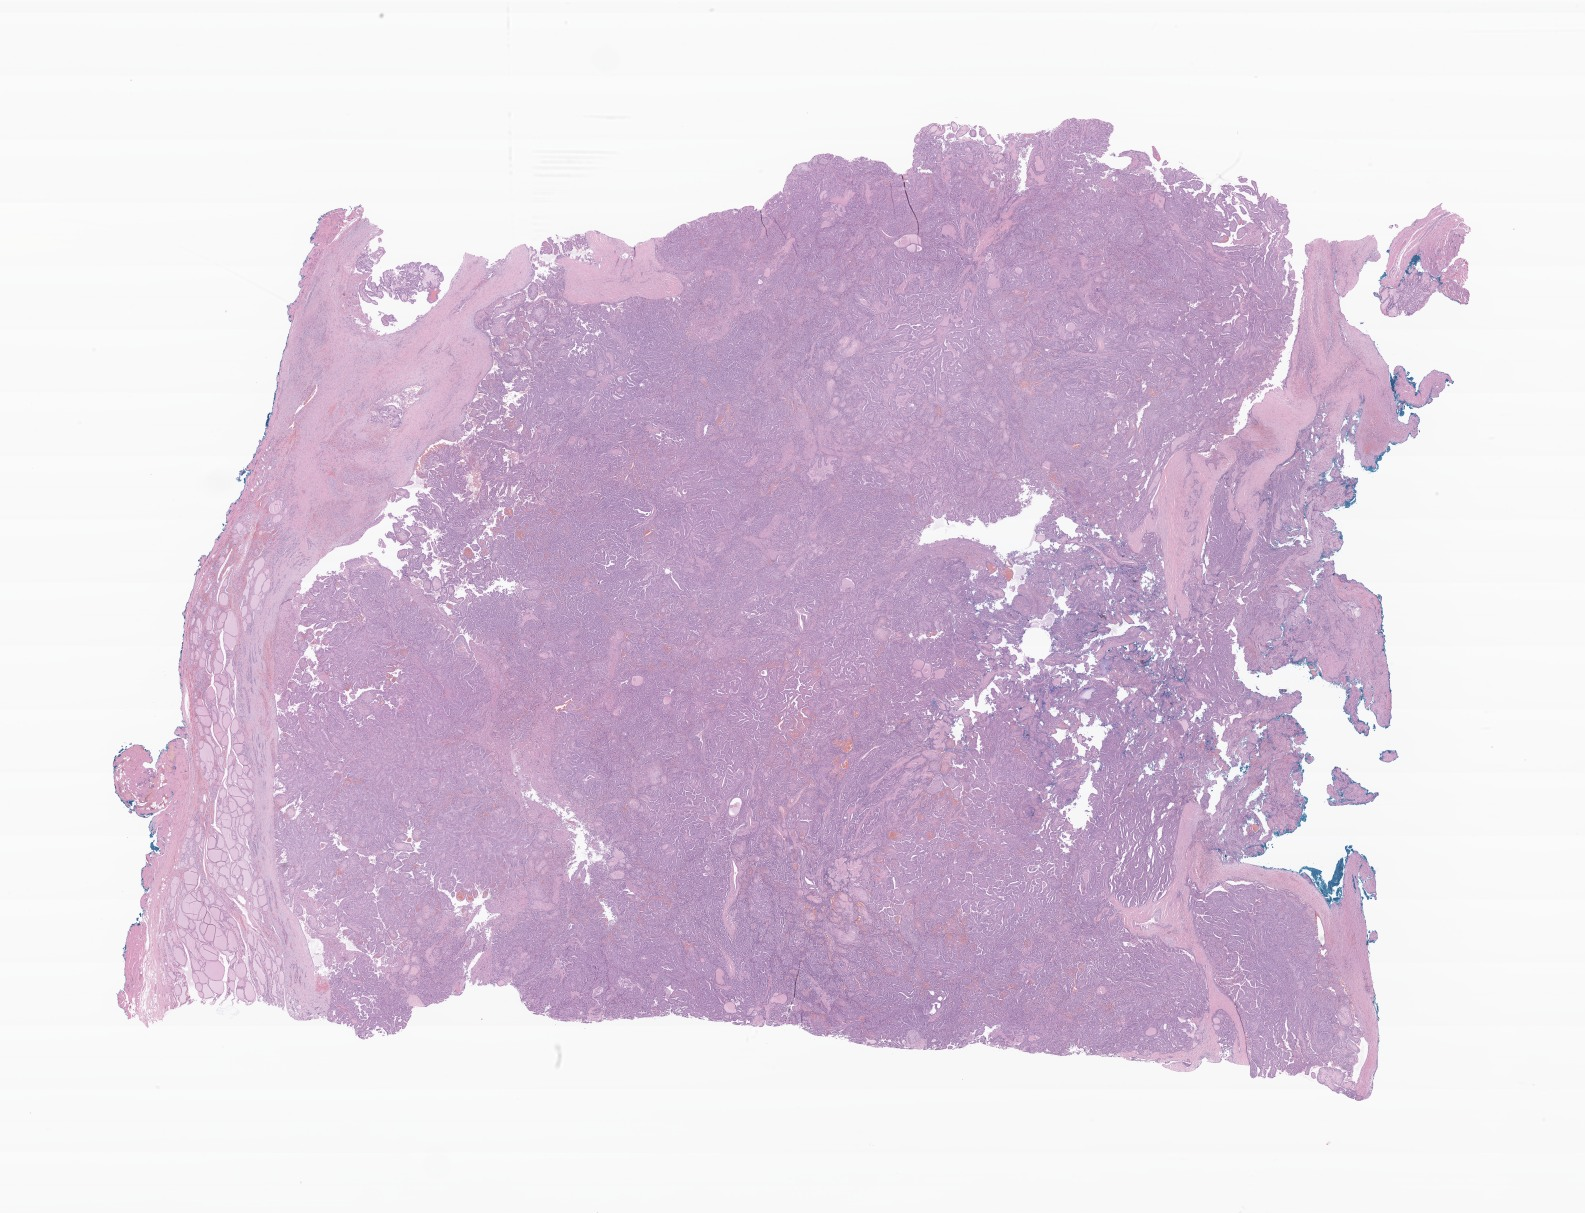
H&E whole-slide image of tumor tissue from the thyroid, low-resolution overview of the scanned area, about 26.7 x 20.4 mm, formalin-fixed paraffin-embedded section. Patient female; age 237 months.
- diagnosis: Papillary carcinoma, NOS